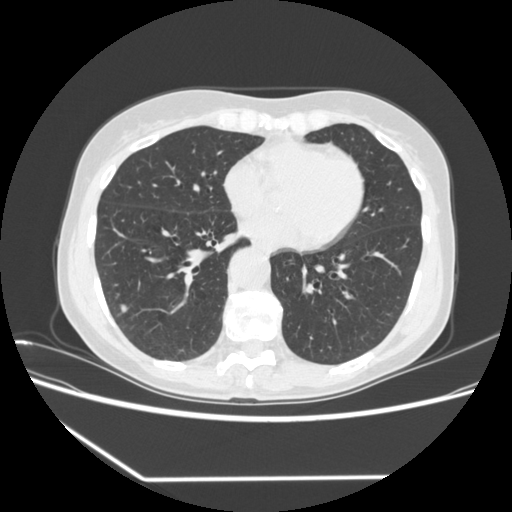
Low-dose screening chest CT, one axial slice. Slice 153 of 323 in the series (ordered by position). 120 kVp. Lung window (W 1500 / L -600 HU). 1.25 mm slice thickness. 512 × 512 image matrix, field of view 360 × 360 mm.
Annotated regions visible in this slice (manually delineated by an expert):
- lesion 2 (nodule, lower lobe of right lung): box from (x=121, y=305) to (x=128, y=313) px